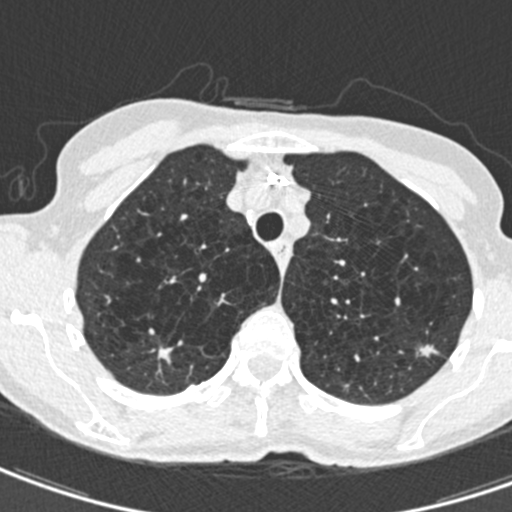
Low-dose screening chest CT, axial slice. Second annual screen. Lung window (W 1500 / L -600 HU). Standard (soft-tissue) reconstruction kernel (B30f). Slice 115 of 498 in the series. 512 × 512 image matrix, field of view 272 × 272 mm. Female, age 71 years at enrolment. Current smoker at enrolment.
• Expert-annotated lung lesion, bounding box <404,332,444,370> (left, top, right, bottom; pixels).
• The screening reader recorded 2 non-calcified nodules or masses ≥4 mm on this exam; which of them this box marks is not recorded.
• Later outcome: lung cancer diagnosed 604 days after this screen (after the third annual screen) — adenocarcinoma, NOS, left upper lobe, moderately differentiated (G2), stage IA (AJCC 6th edition), 12 mm at pathology.